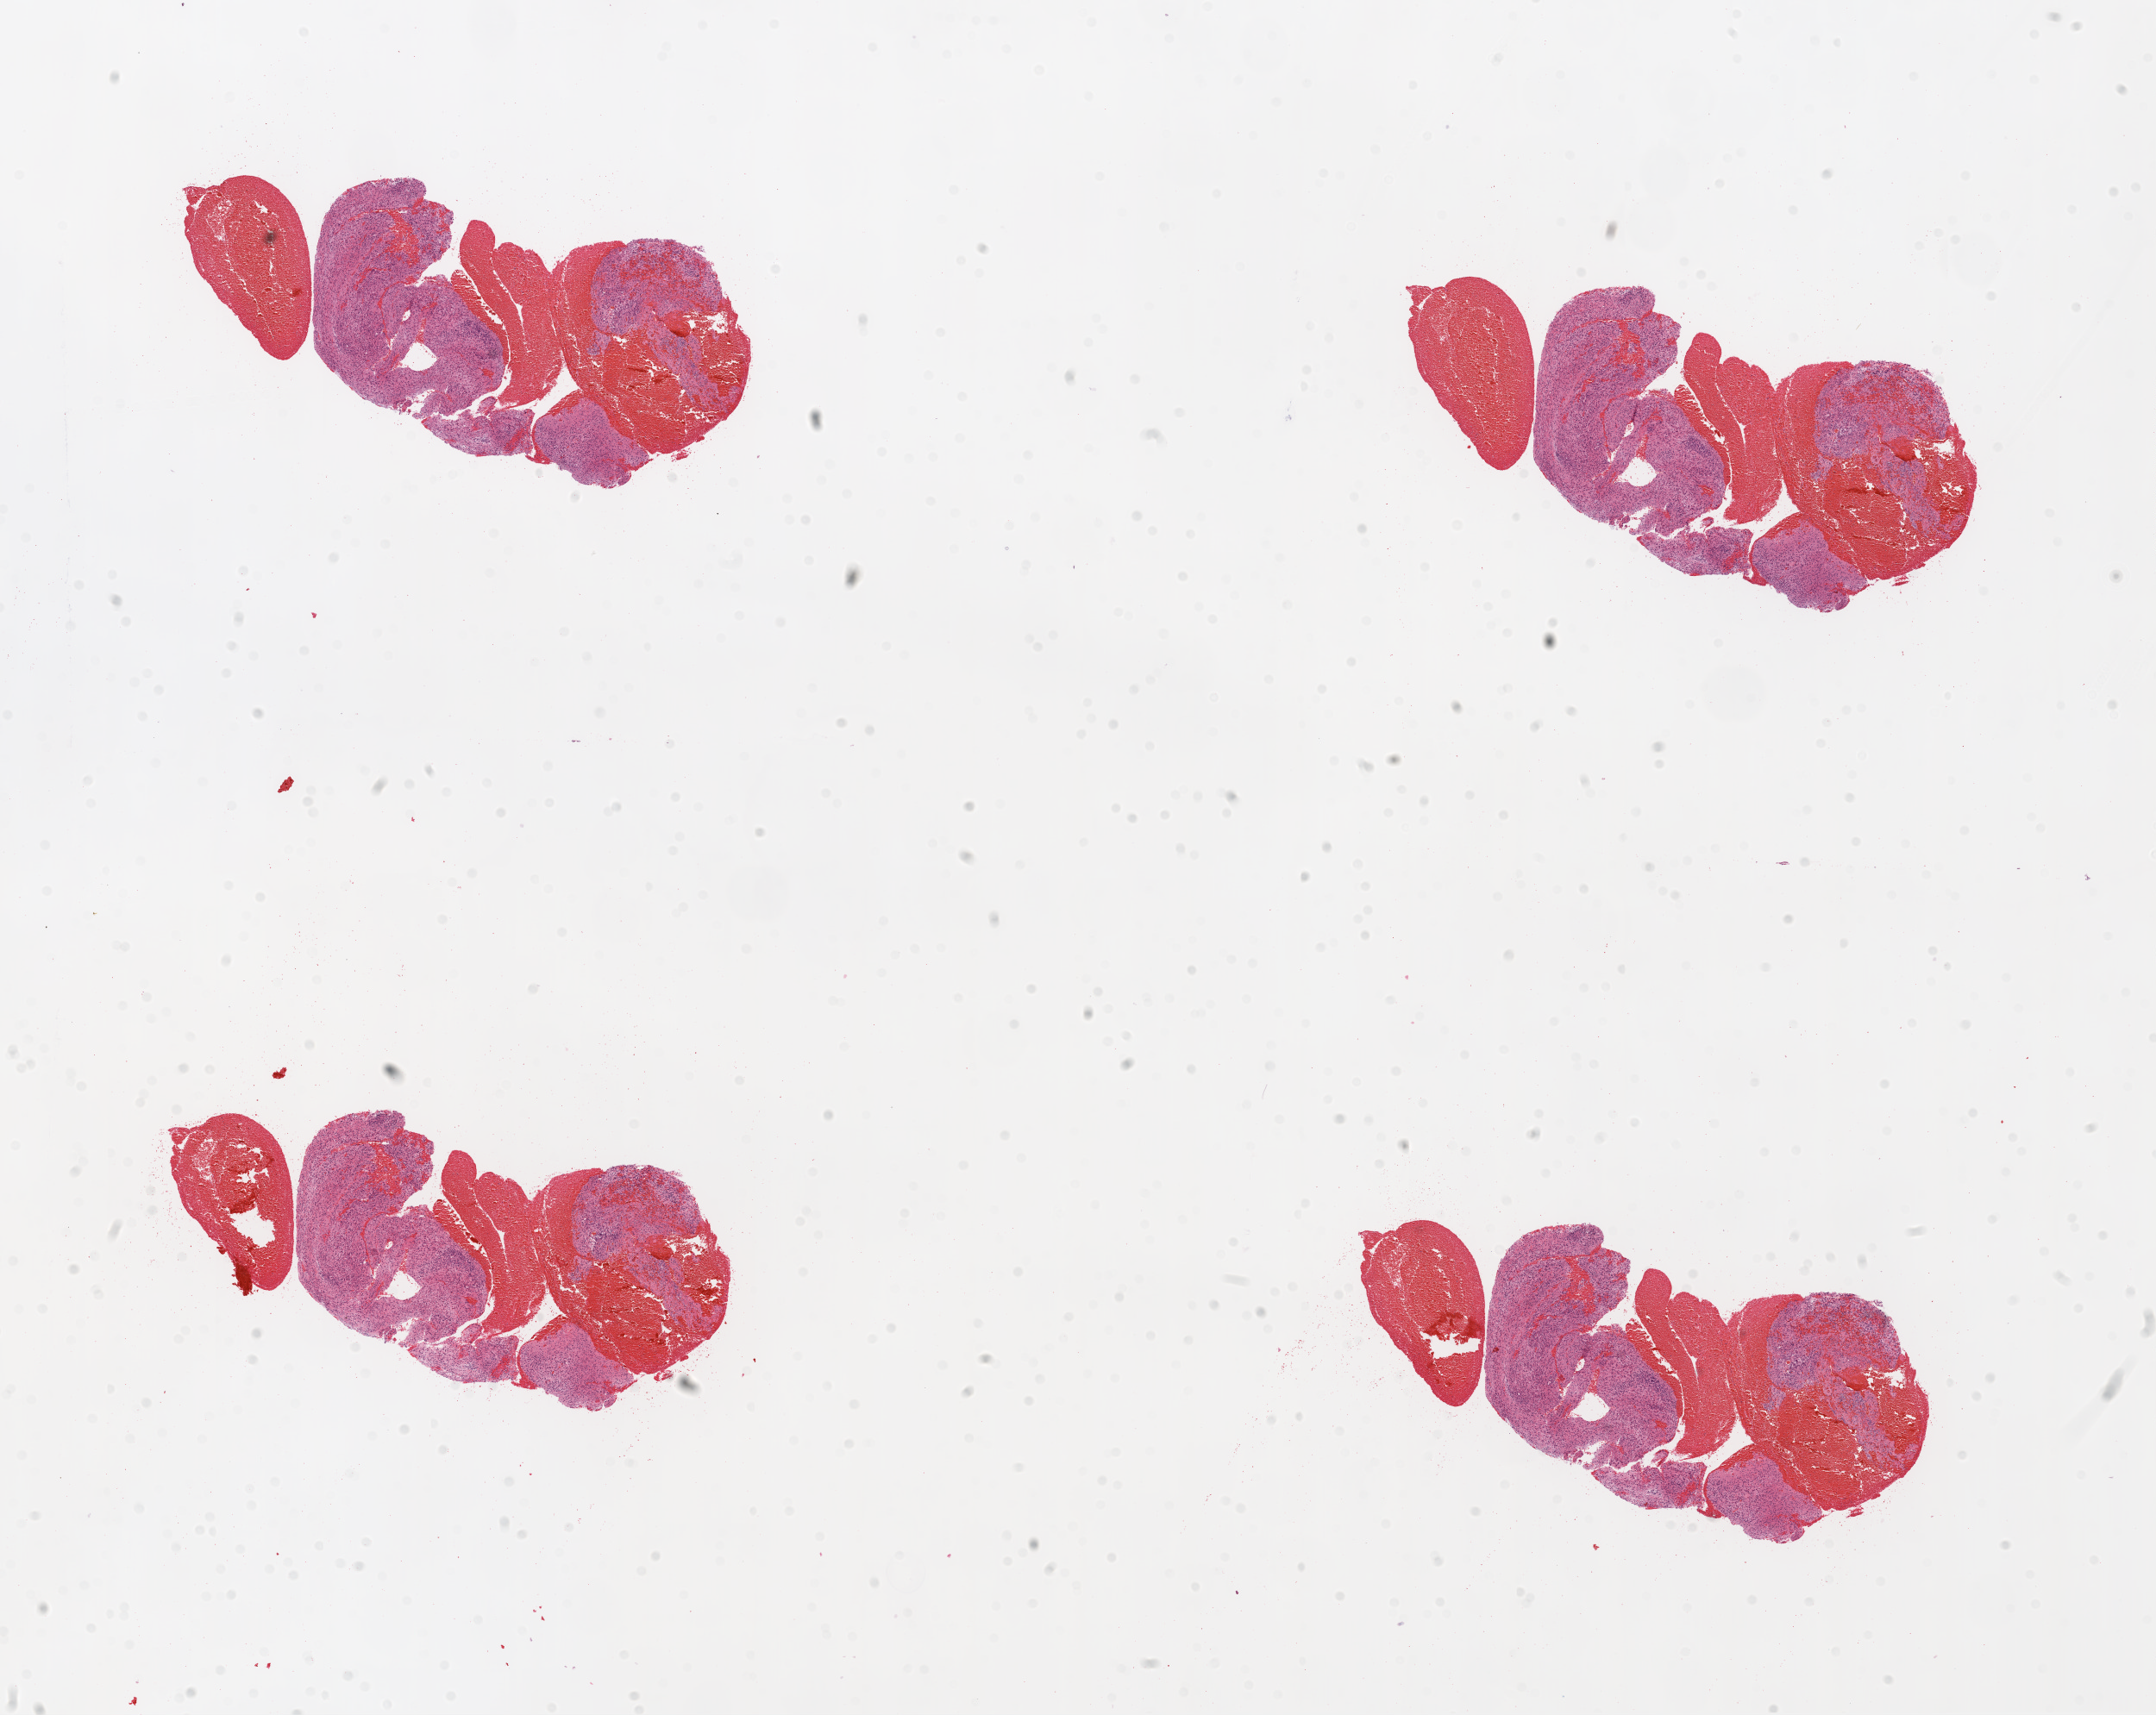
H&E-stained whole-slide image, low-resolution overview of the scanned area, about 20.1 x 16.0 mm; FFPE section; primary tumour sample from the brain. Male patient; age at initial diagnosis 43 years.
Diagnosis: Glioblastoma.